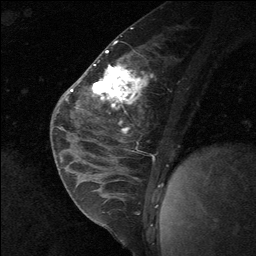
Breast MRI (dynamic contrast-enhanced), one sagittal slice. Slice 30 of 64 in the series (ordered by position). Dynamic contrast-enhanced study with each time point stored as its own series, time point 2 of 3 at this slice position (early post-contrast, ordered by acquisition time). 1.5 T. TE 4.8 ms, TR 27 ms. 256 × 256 image matrix. Patient: female, 26 years. From the clinical record (not read from this slice): setting: breast cancer imaged before/during neoadjuvant chemotherapy; receptor status: HR-positive, HER2-negative.
Structures marked on this image (semi-automatically segmented with operator editing):
- analysis volume of interest (the breast-tissue region the enhancement analysis was run in; not a lesion): bounding box <86,43,130,138> (left, top, right, bottom; pixels)
- tumour enhancement mask (voxels above the 90 % enhancement threshold inside the analysis volume of interest): <92,70,115,95>